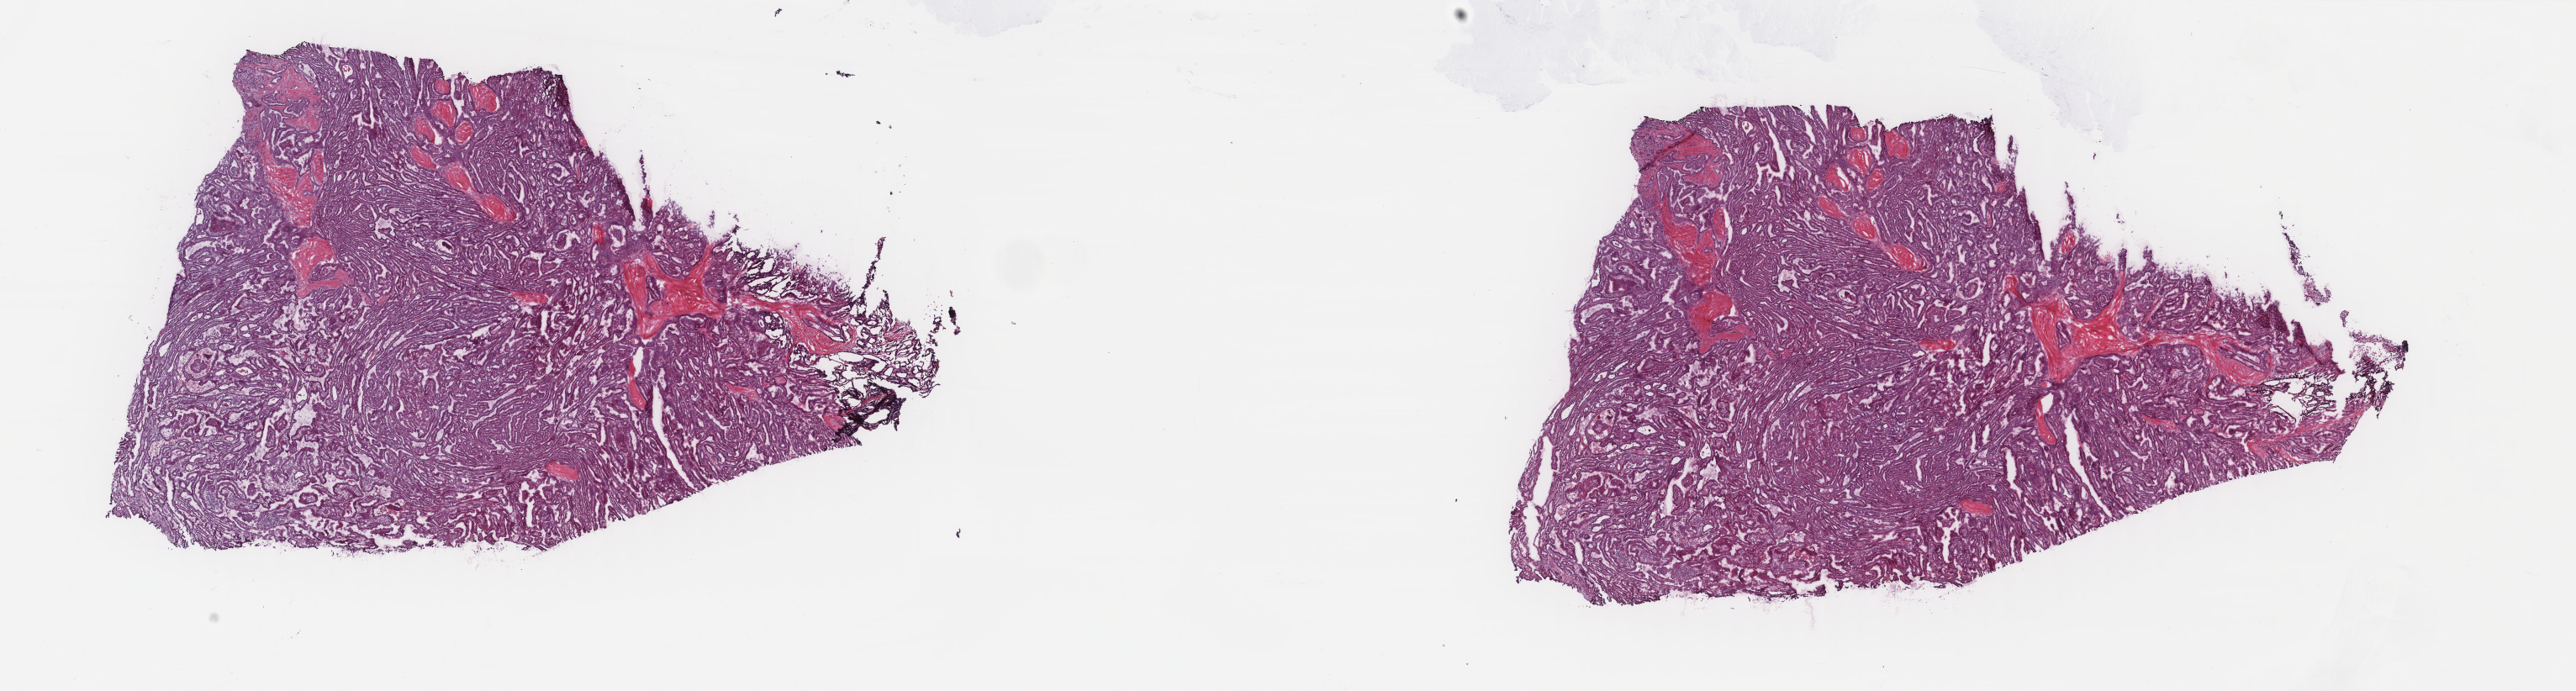
Whole-slide histology image, H&E — a low-resolution overview of the entire scanned area, about 24.3 x 6.5 mm (slide scanned at 40x), frozen section from the top of the tissue portion, primary tumour sample from the thyroid. Patient: female, age at initial diagnosis 55 years. Composition of this section per pathologist review: tumour cells 85%, tumour nuclei 85%, normal cells 0%, stromal cells 15%, necrosis 0%. Infiltration values recorded for this section: lymphocyte infiltration 3%, monocyte infiltration 0%, neutrophil infiltration 0%.
Histologic diagnosis: Papillary carcinoma, columnar cell (thyroid gland). AJCC pathologic stage: I (7th edition).